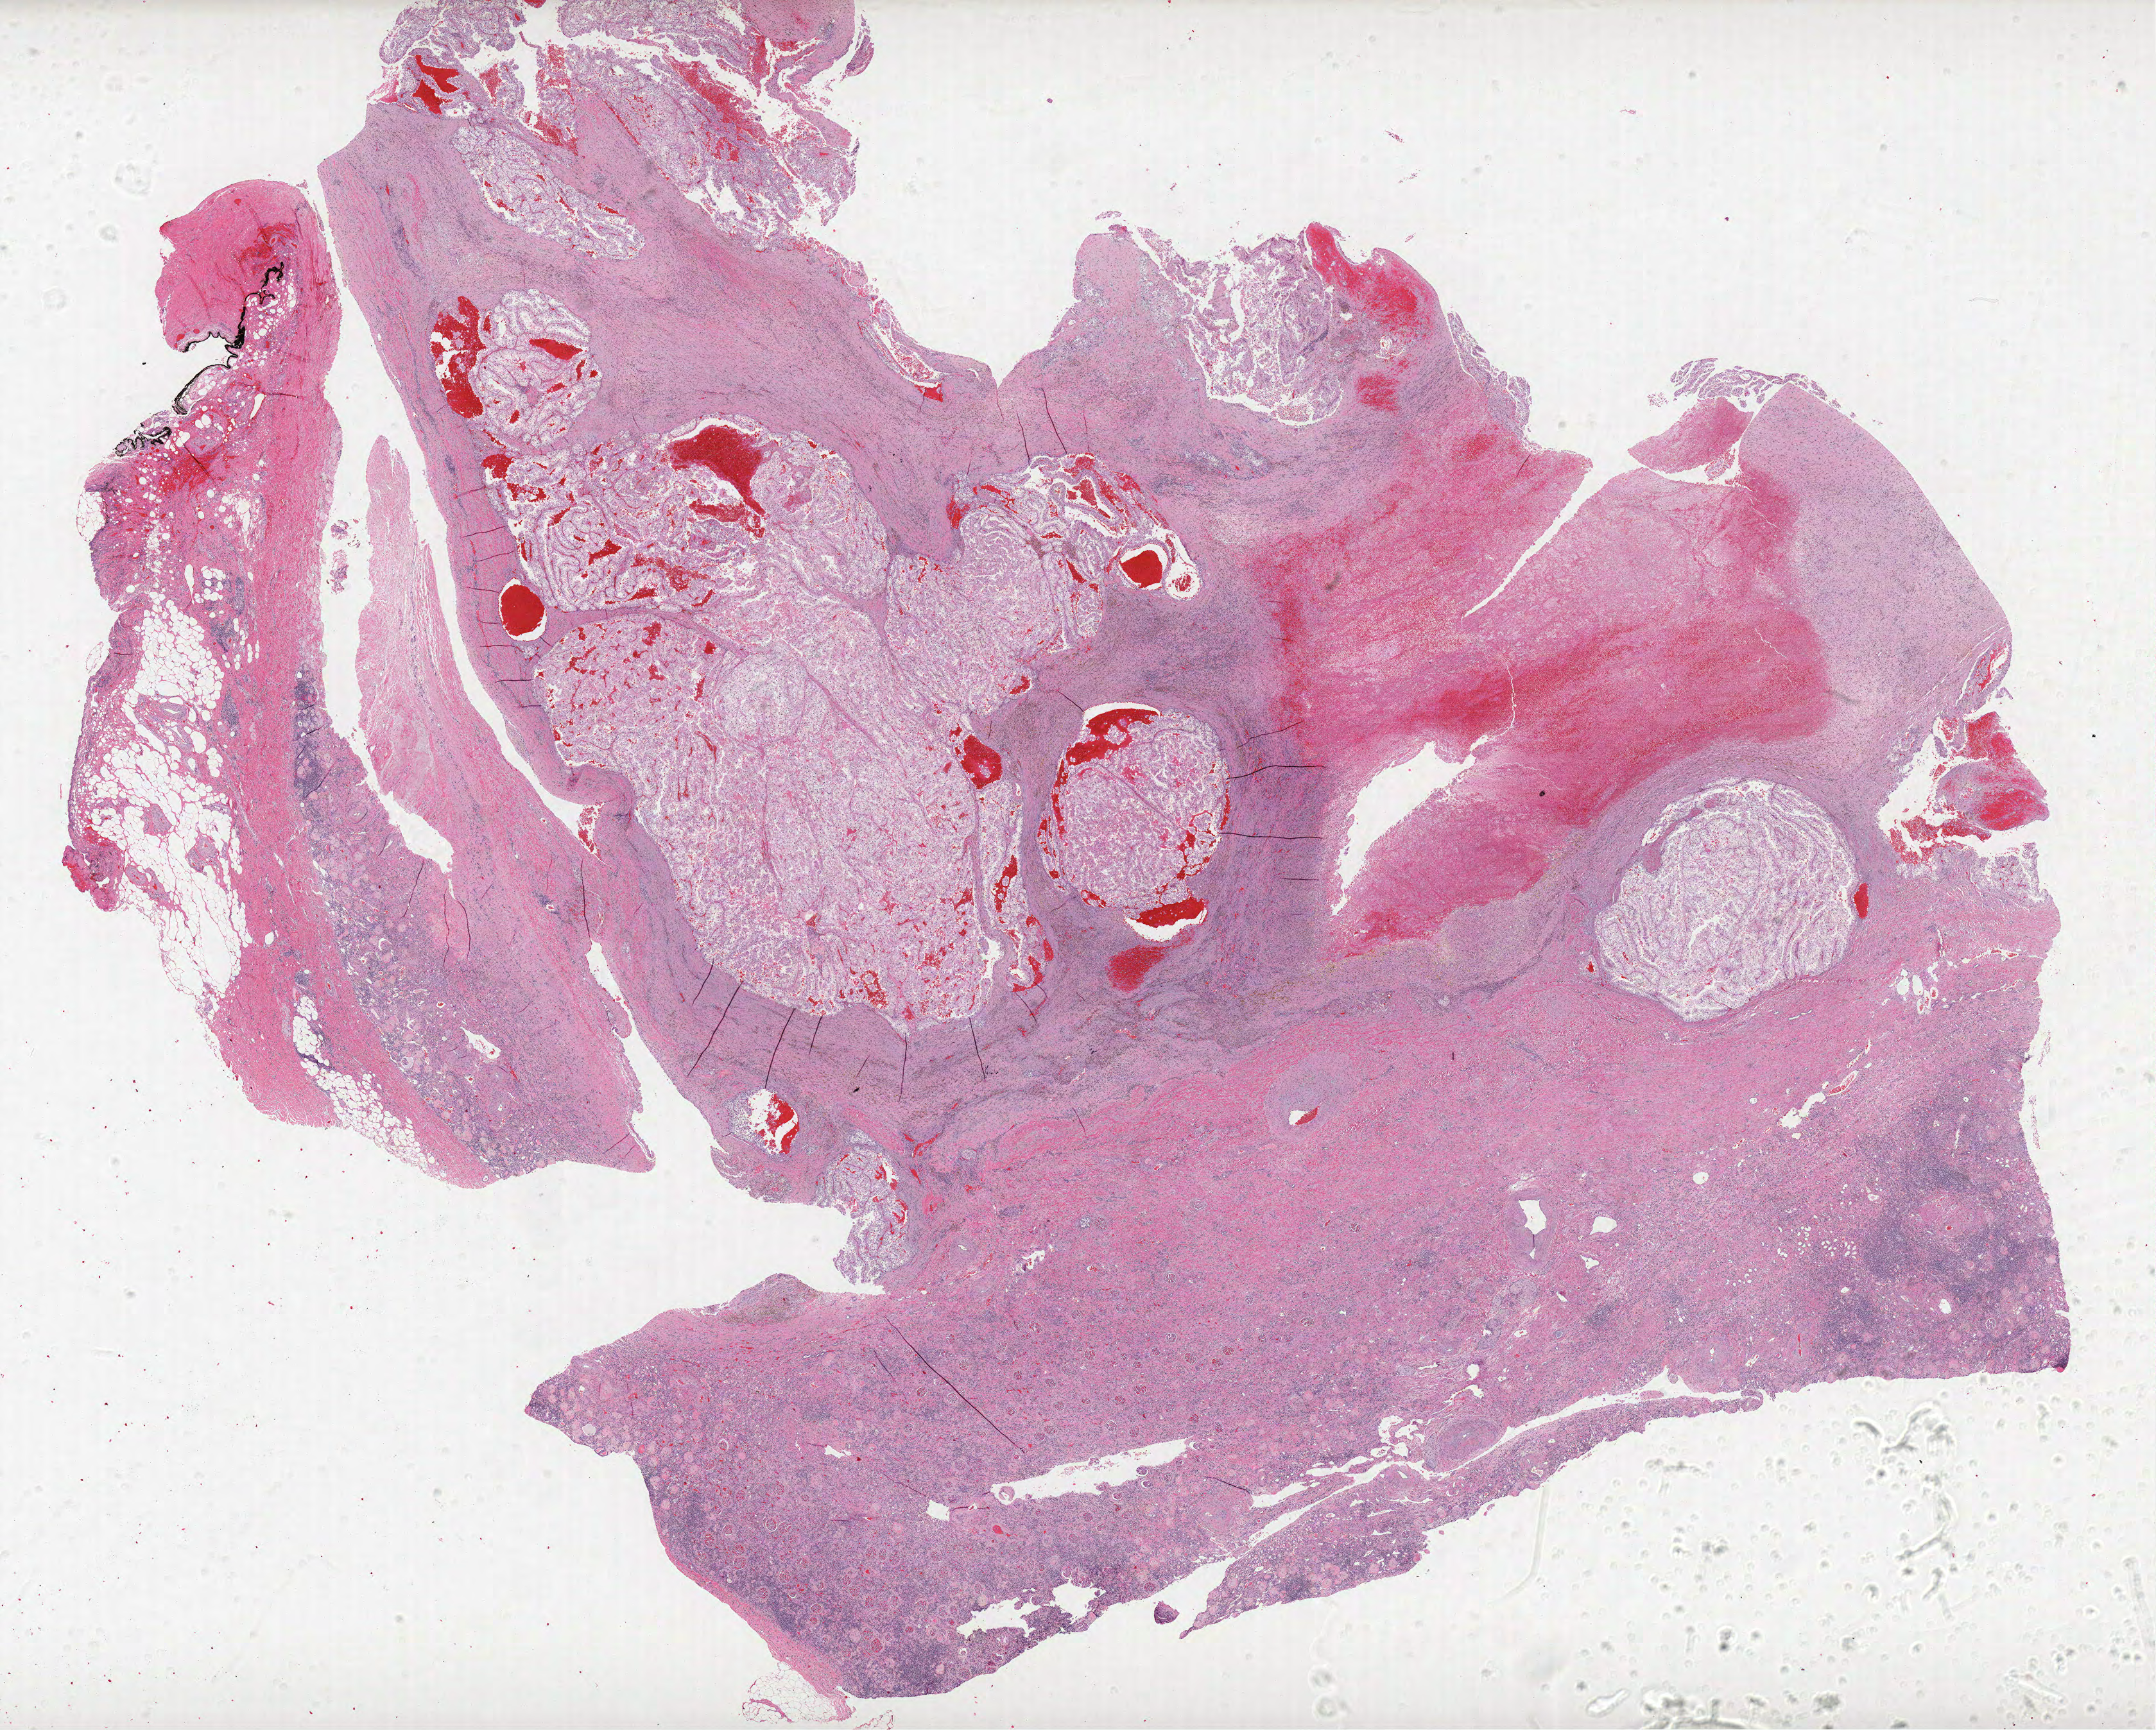
Whole-slide histology image, H&E-stained, shown as a low-resolution overview of the whole scanned area (about 26.9 x 21.6 mm, slide scanned at 40x); FFPE section; primary tumour sample from the kidney. Patient: male, age at initial diagnosis 54 years.
Histologic diagnosis: Papillary adenocarcinoma, NOS. AJCC pathologic stage: III (6th edition). Laterality: right.